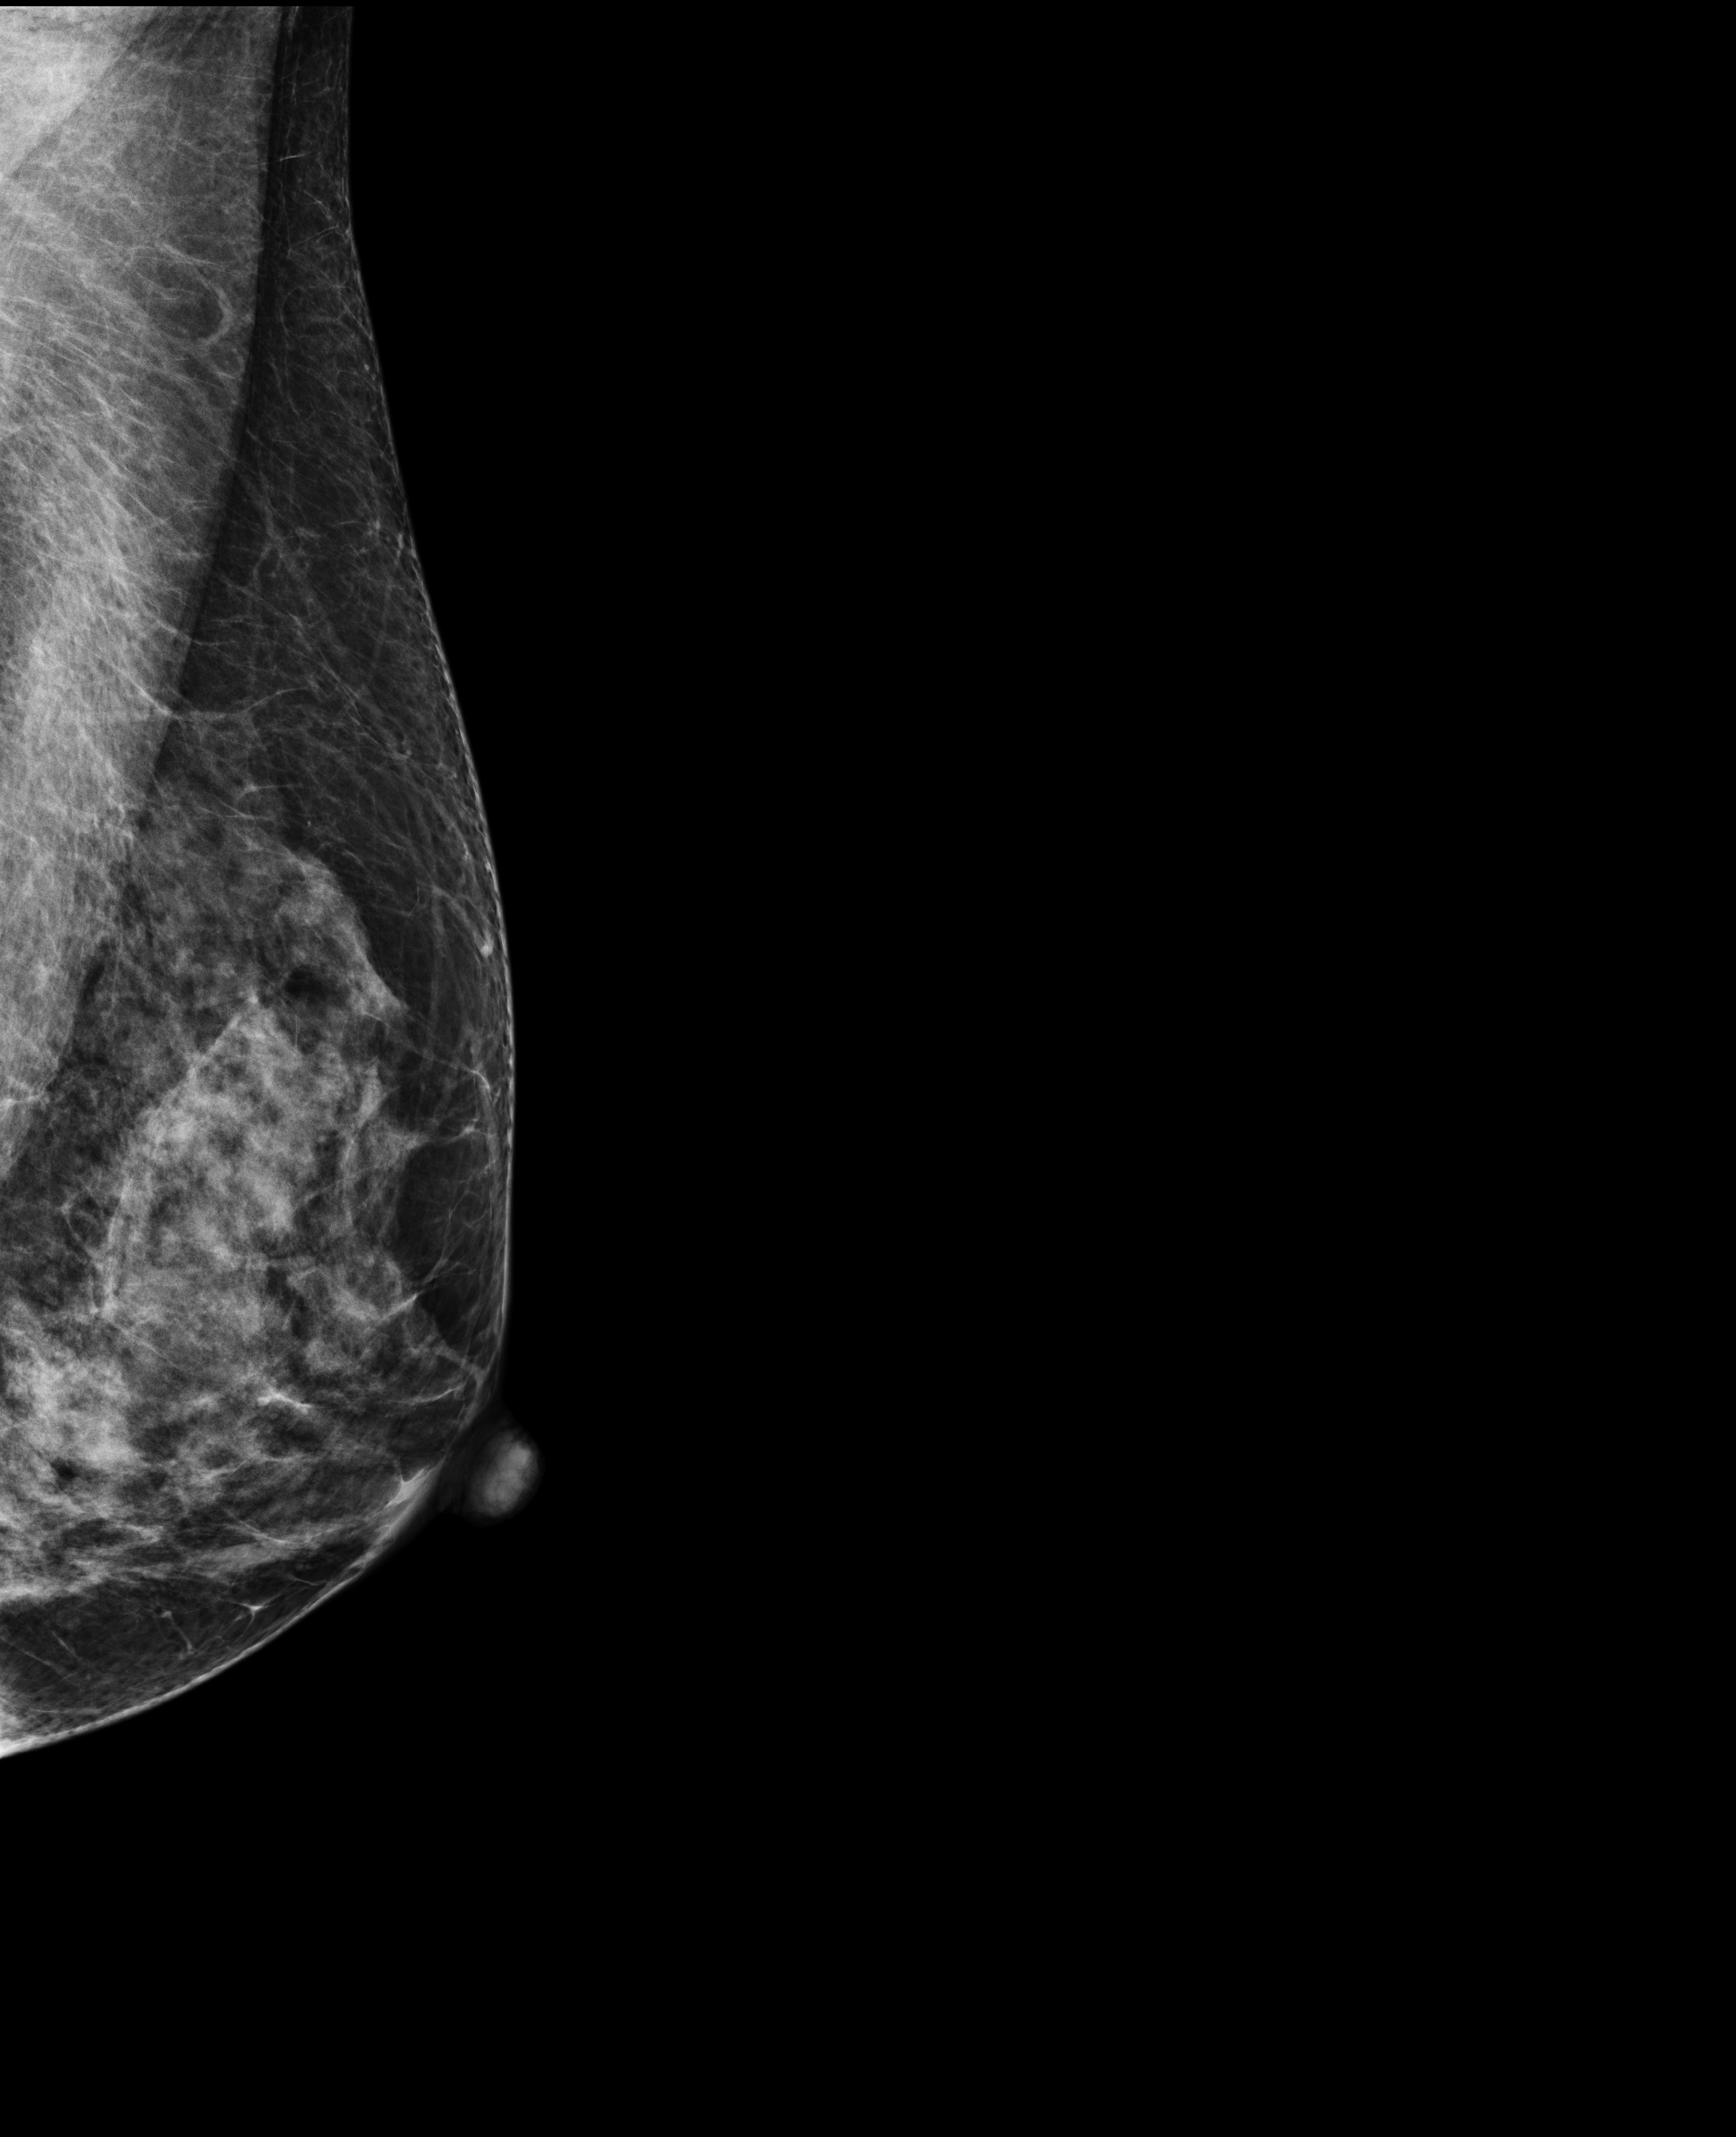
Screening examination. Female patient, age 42 years.
Image type: full-field digital mammogram. Breast: left. Projection: laterally exaggerated craniocaudal (XCCL) view.